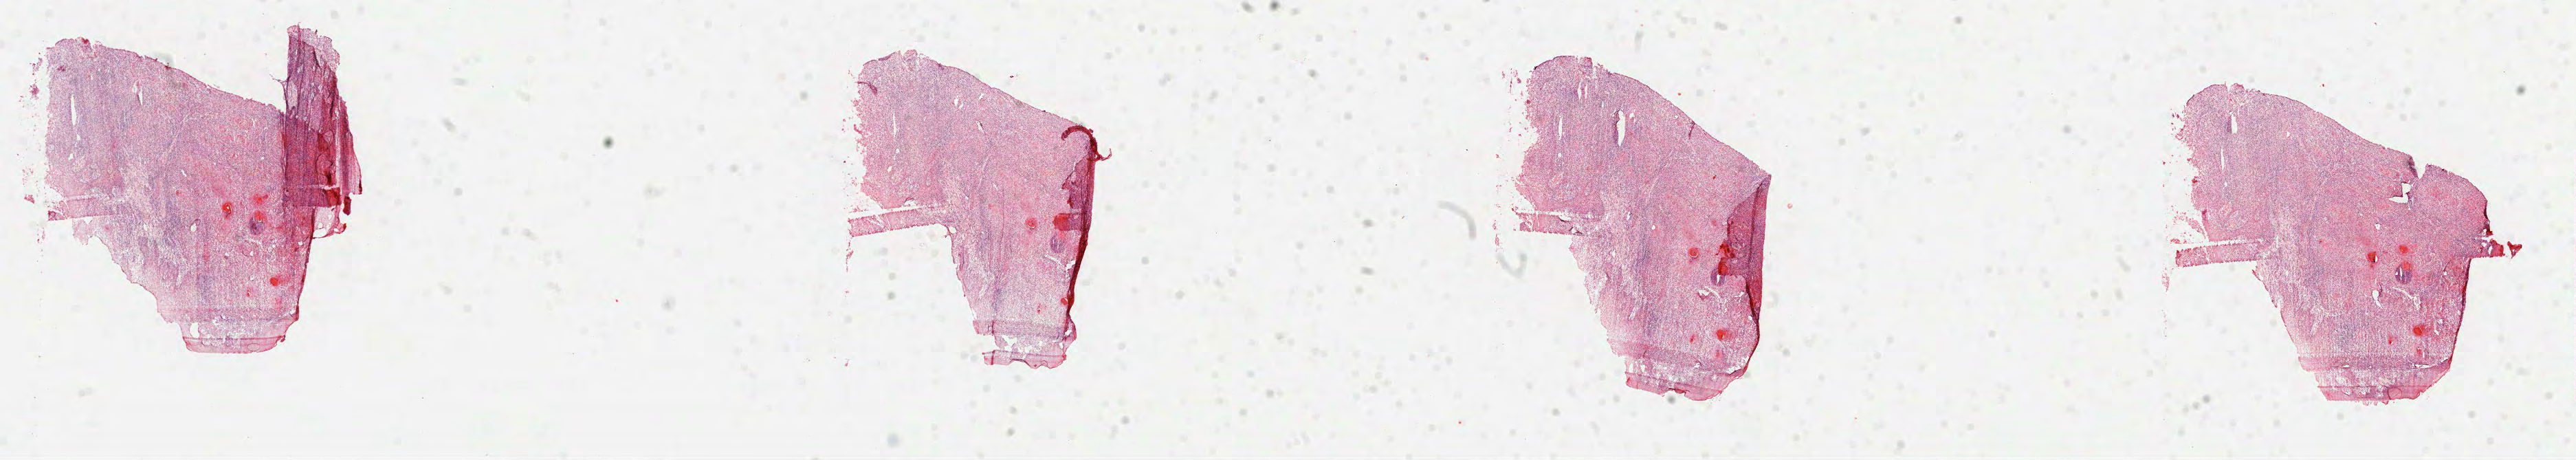
Whole-slide histology image, Hematoxylin and eosin (H&E) stained — a low-resolution overview of the entire scanned area, about 30.2 x 5.4 mm. FFPE section. Primary tumour sample from the head and neck. Male patient; age at initial diagnosis 73 years. Histologic grade: G2 (moderately differentiated).
AJCC pathologic stage: I (7th edition). Lymph nodes positive (case pathology): 0 of 9 examined. Pathologic diagnosis: Squamous cell carcinoma, NOS. TNM: T1 N0.